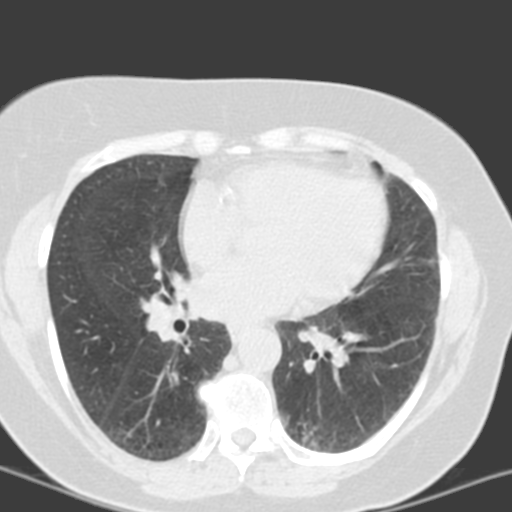
Low-dose screening chest CT, axial slice. Third screening round (two years after baseline). Lung window (W 1500 / L -600 HU). Standard (soft-tissue) reconstruction kernel (B). Slice 75 of 150 in the series. Female participant, aged 55 years at enrolment.
• Lesion marked by an expert reader, box from (x=274, y=402) to (x=357, y=460) px.
• The screening reader recorded 6 non-calcified nodules or masses ≥4 mm on this exam (left lower lobe, left lower lobe, left upper lobe, lingula, lingula, right middle lobe); which of them this box marks is not recorded.